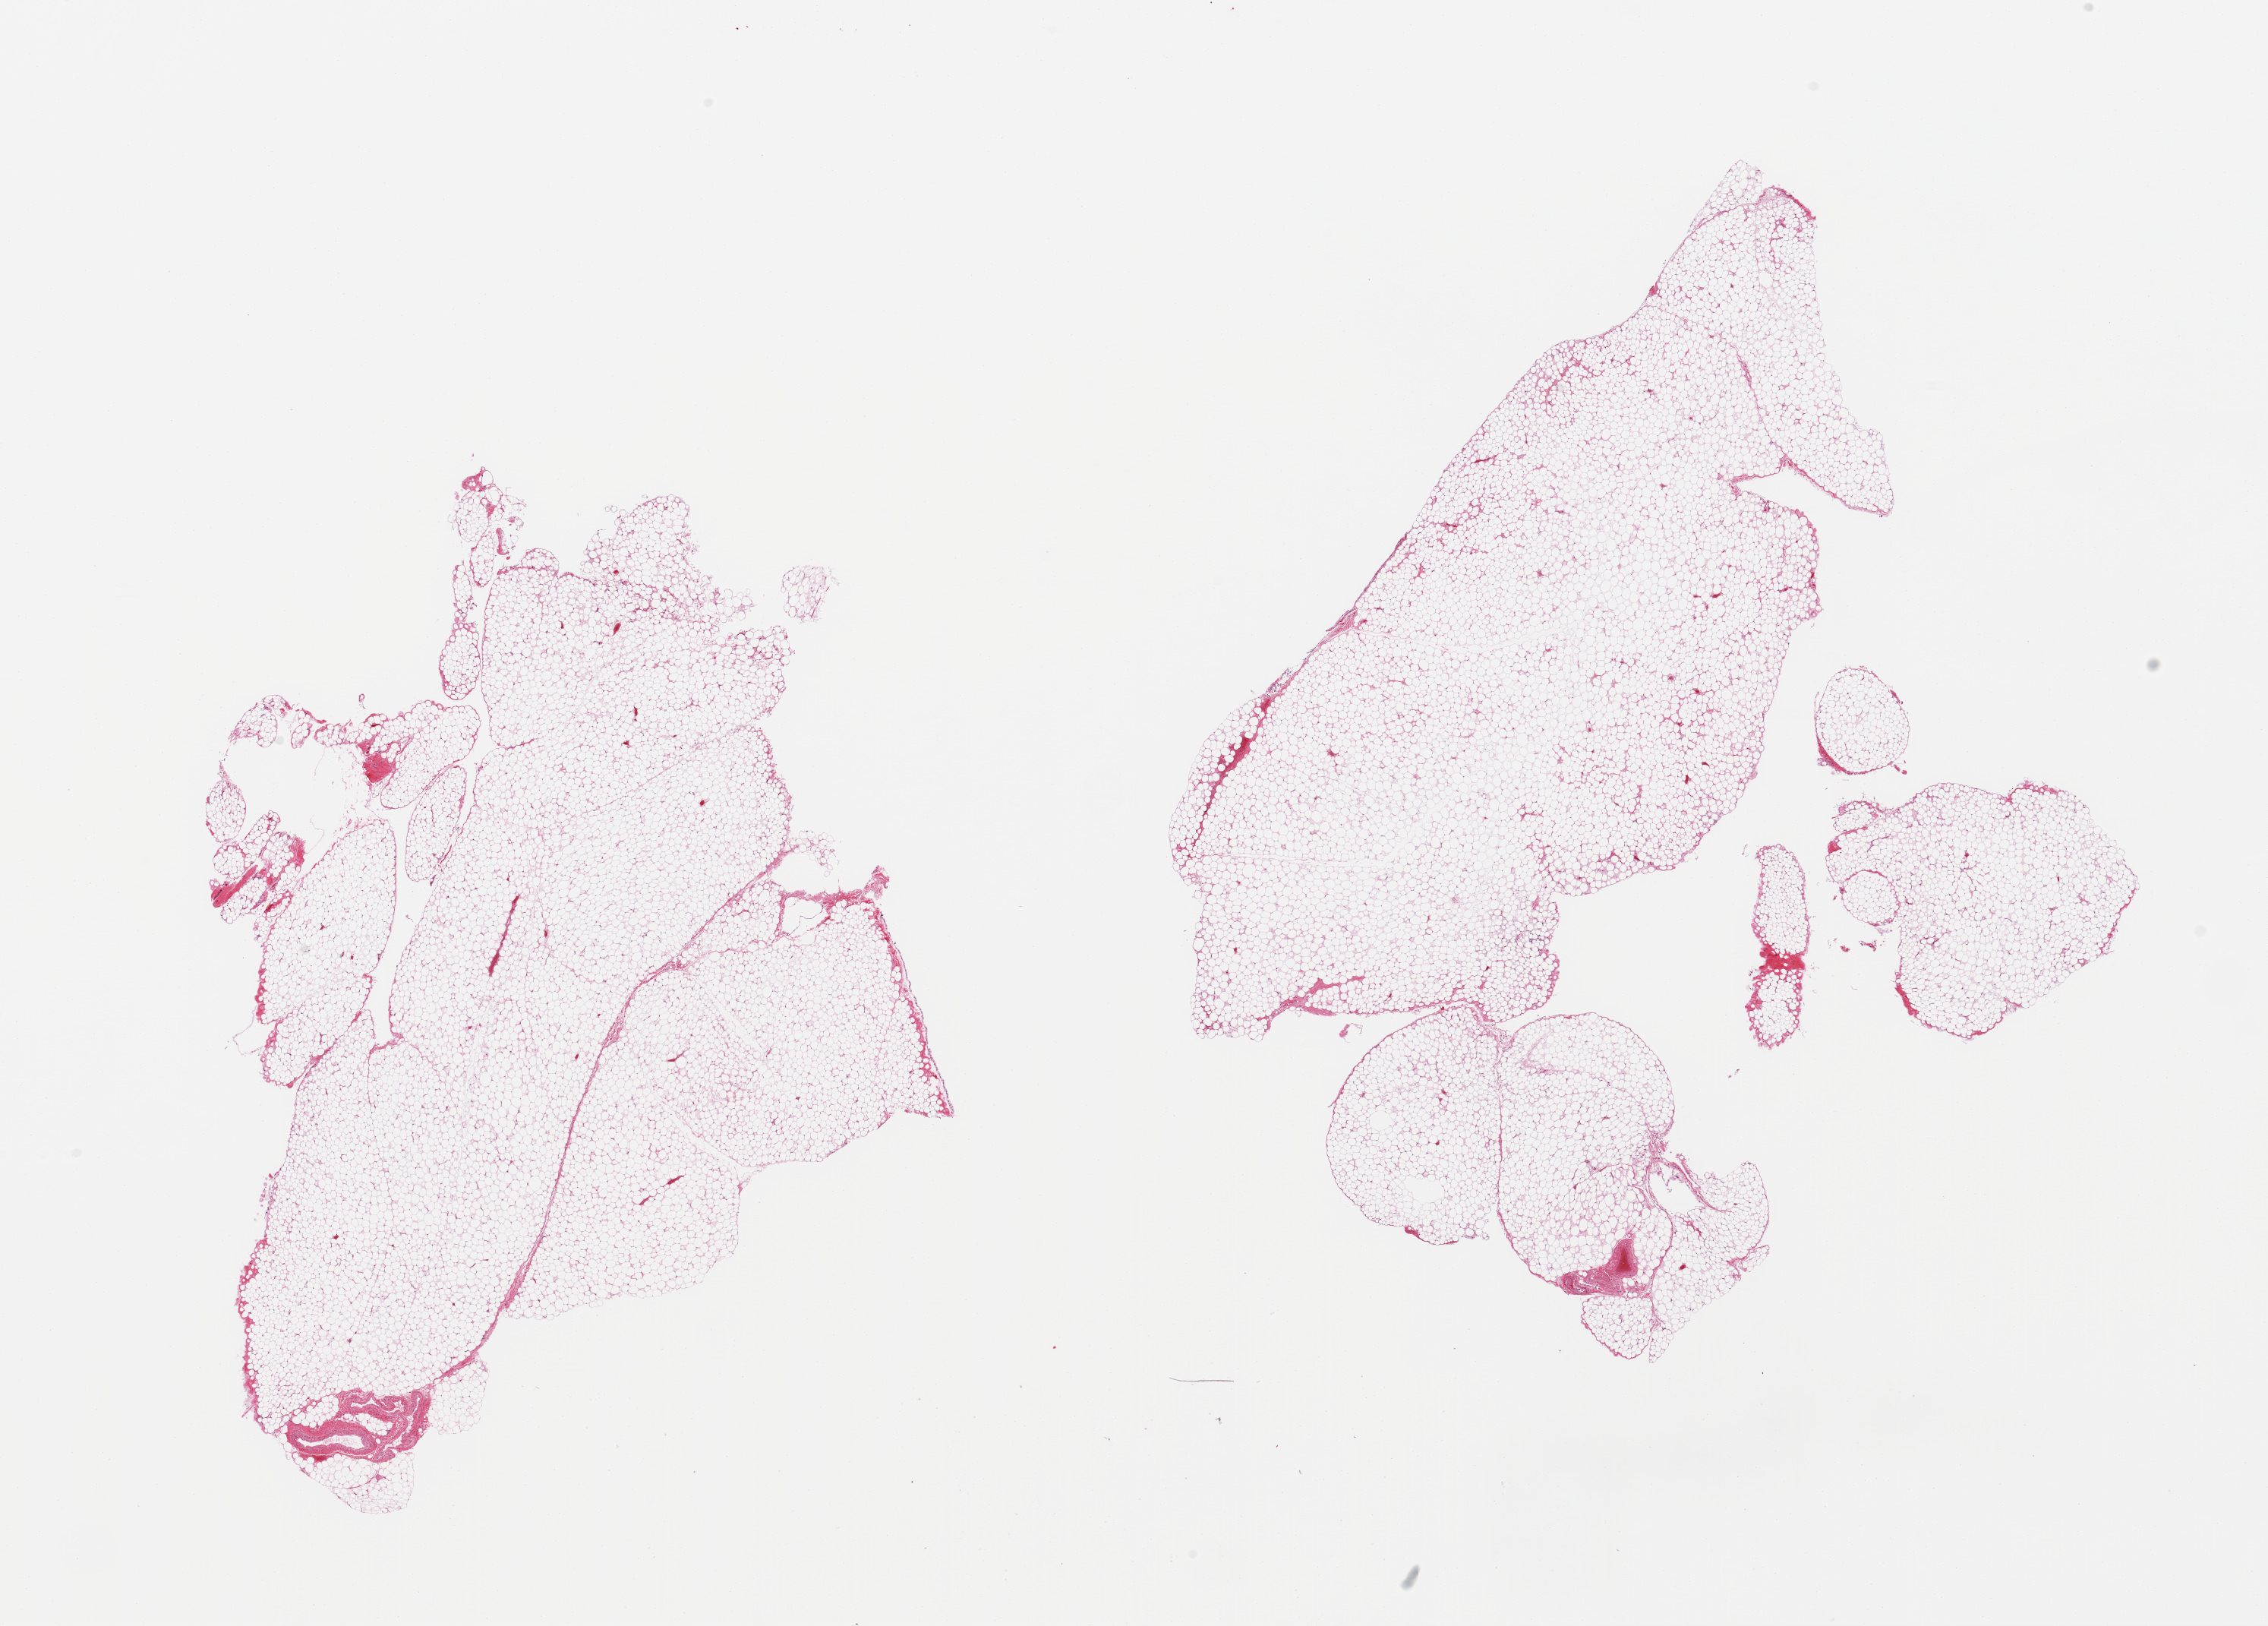
Digitized hematoxylin and eosin (H&E)-stained section, low-resolution overview of the scanned area, about 23.6 x 16.9 mm; PAXgene-fixed paraffin-embedded (PFPE) section; target tissue: omentum; tissue donor sample.
Pathologist's review note for this sample: 2 pieces; minimal fibrous content.